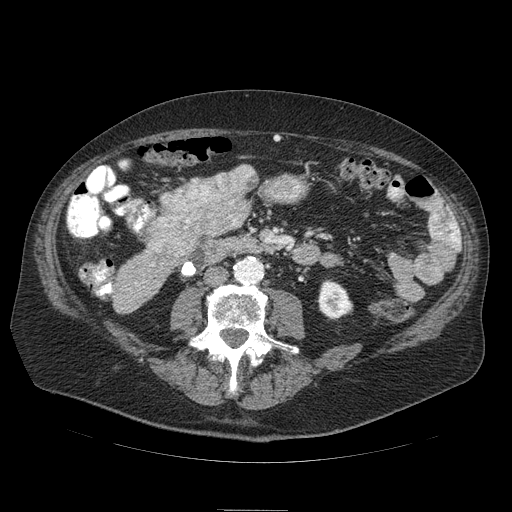
Contrast-enhanced abdominal CT (liver protocol), one axial slice; slice 13 of 103 in the series (ordered by position); reconstruction kernel STANDARD; 120 kVp; soft-tissue window (W 400 / L 40 HU); 2.5 mm slice thickness; 512 × 512 image matrix, field of view 440 × 440 mm. Case-level facts recorded for this patient, not image findings: diagnosis: hepatocellular carcinoma (patient treated with transarterial chemoembolisation; whether this scan precedes or follows treatment is not stated here); TNM stage (as recorded): Stage-IIIA; Child-Pugh class: B; tumour differentiation: well differentiated; tumour size: 13 cm.
Outlined on this slice (semi-automatic segmentation, software-assisted and operator-edited):
- mass: bounding box (x1, y1, x2, y2) in pixels: (147, 164, 258, 257)